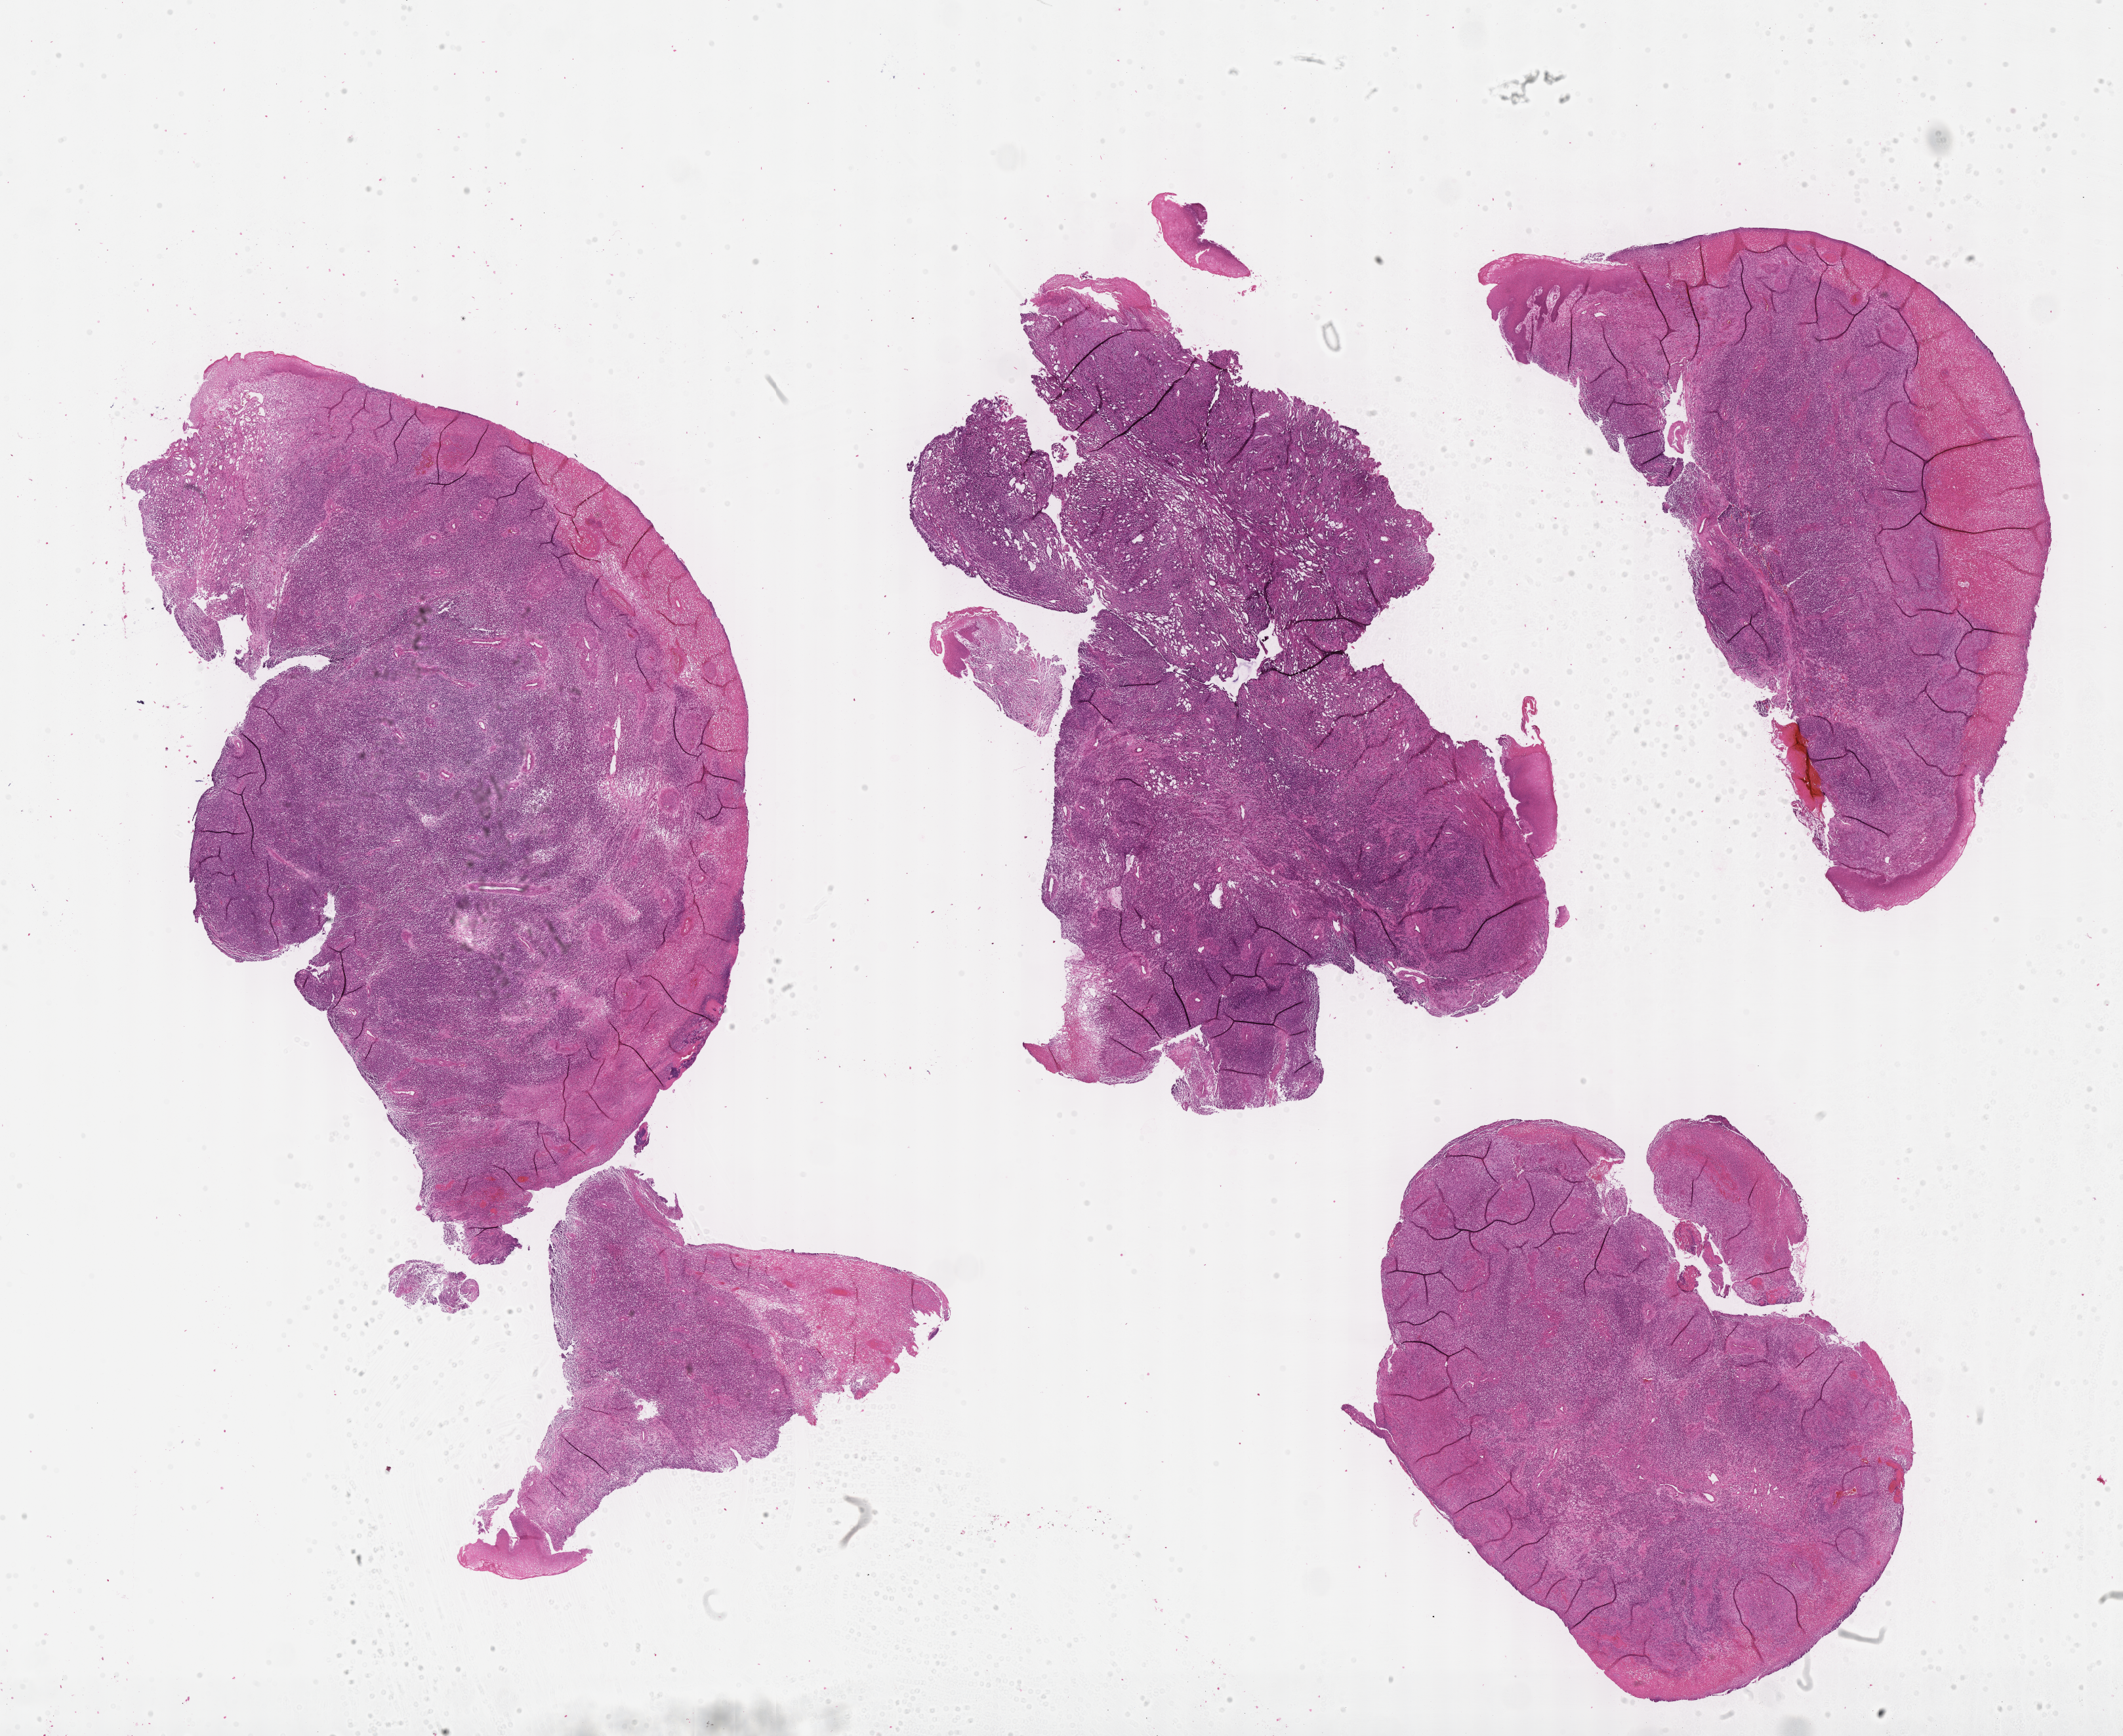
Digitized hematoxylin and eosin (H&E)-stained section of tumor tissue, whole scanned area (about 26.2 x 21.4 mm) shown as a low-resolution overview. Formalin-fixed paraffin-embedded section. Sample anatomic site: soft tissue, cheek-right. Patient: male, age 11.5 years at diagnosis.
Metastatic status at presentation (as recorded): non-metastatic (unconfirmed). Diagnosis: rhabdomyosarcoma; histological classification: embryonal rhabdomyosarcoma. Stage (as recorded): 1.